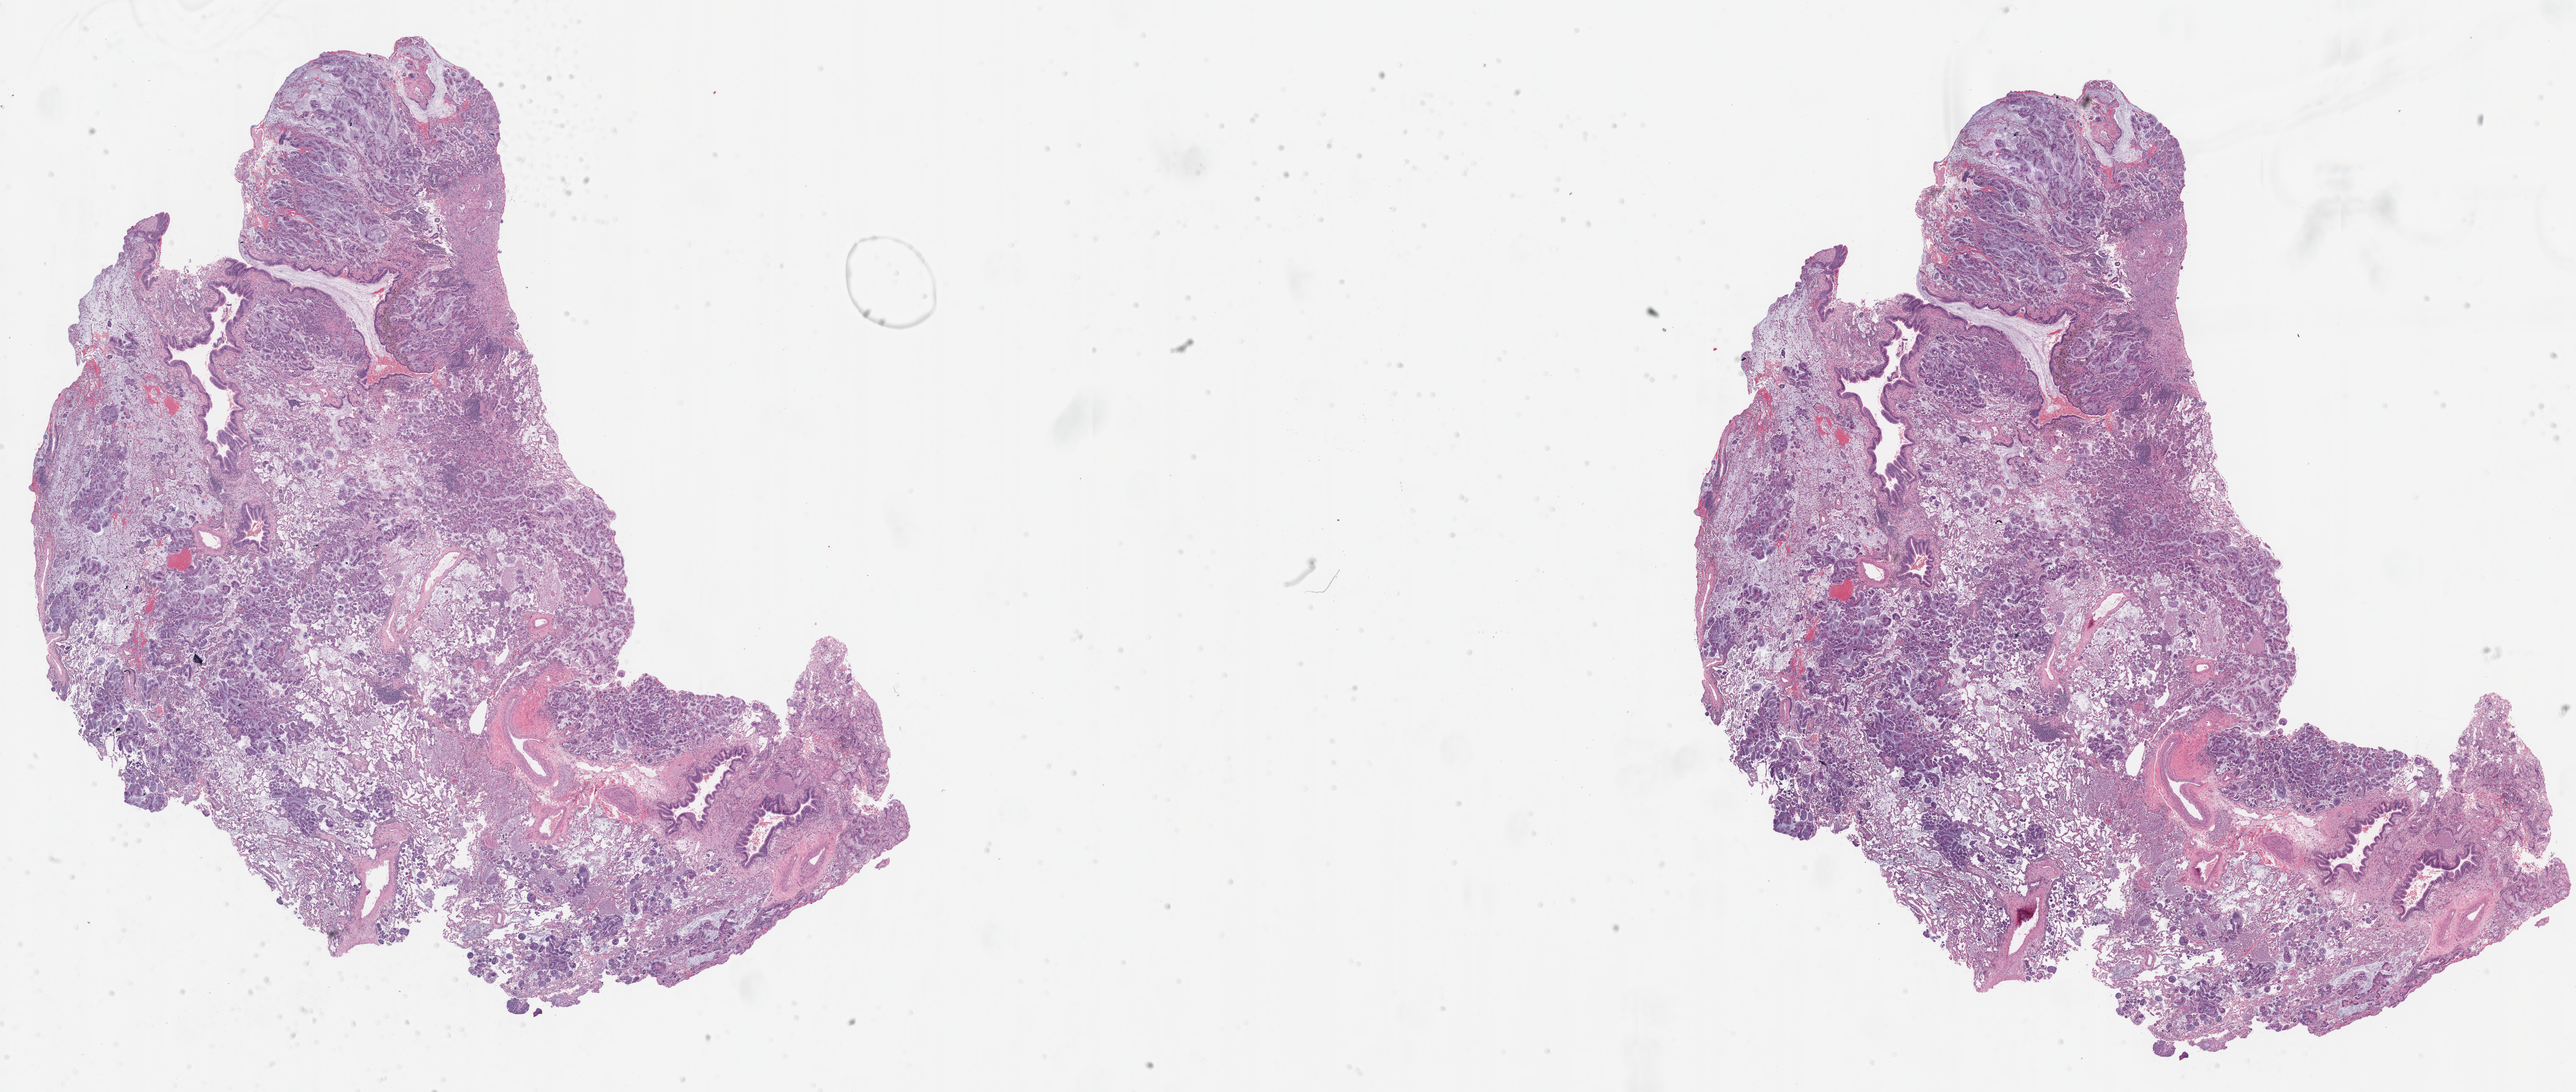
Hematoxylin and eosin (H&E) stained whole-slide image — a low-resolution overview of the entire scanned area, about 33.0 x 14.0 mm (slide scanned at 20x); formalin-fixed paraffin-embedded (FFPE) diagnostic section; sample: primary tumour, lung. Patient sex: male.
Diagnosis: Adenocarcinoma, NOS (lower lobe, lung).